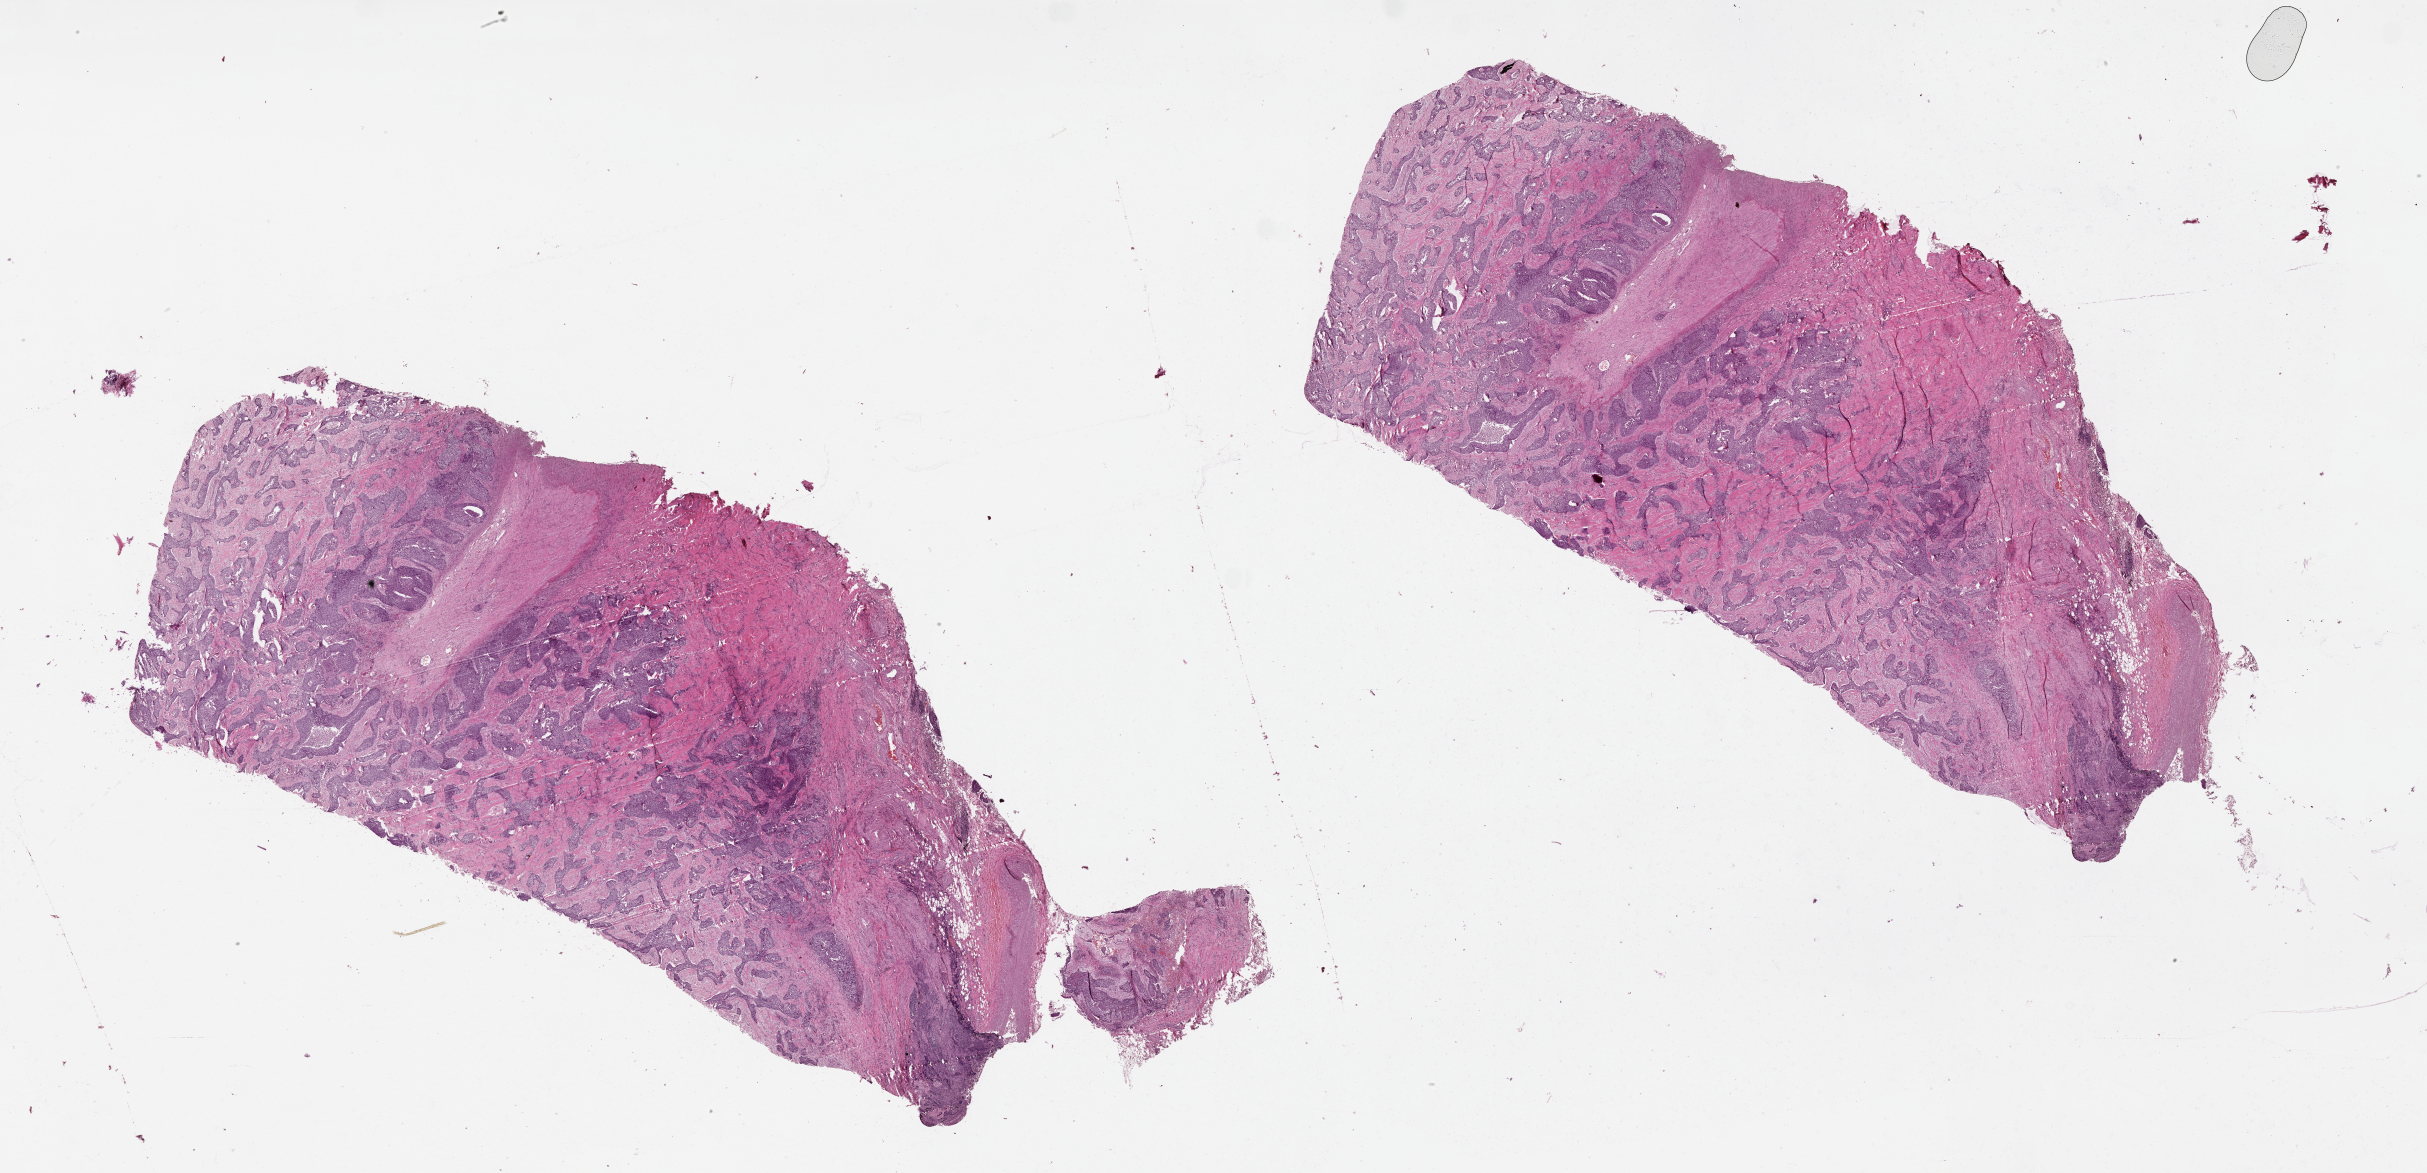
H&E-stained whole-slide image, a low-resolution overview of the entire scanned area, about 39.1 x 18.9 mm. Lung, tumour tissue. Patient: male, age 63 years.
Patient diagnosis (cohort enrolment): squamous cell carcinoma (lung).